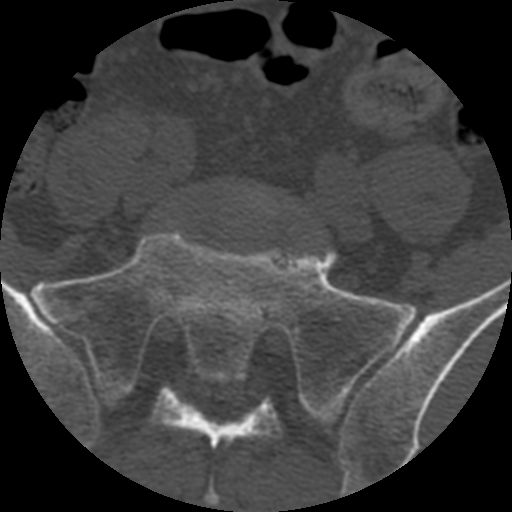
CT including the spine, one axial slice; position 233 of 399 along the scan axis; reconstruction kernel STANDARD; 120 kVp; bone window (W 1800 / L 400 HU); 1.25 mm slice thickness; 512 × 512 image matrix, field of view 160 × 160 mm. Patient age 71 years. Case-level facts recorded for this patient, not image findings: primary cancer: prostate.
Outlined on this slice (semi-automatically segmented with operator editing):
- L5 vertebra: bounding box (x1, y1, x2, y2) in pixels: (249, 186, 278, 215)